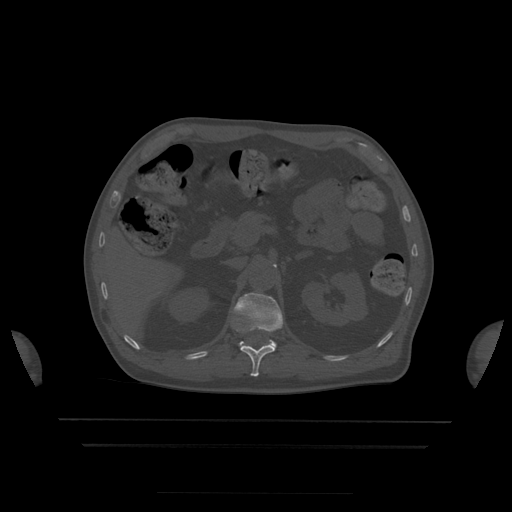
CT including the spine, one axial slice. Bone window (W 1800 / L 400 HU). 1.25 mm slice thickness. 512 × 512 image matrix, field of view 436 × 436 mm. Patient age 68 years. Case-level facts recorded for this patient, not image findings: primary cancer: urothelial.
Annotated regions visible in this slice (semi-automatic segmentation, software-assisted and operator-edited):
- L1 vertebra: bounding box [x1, y1, x2, y2] px = [232, 293, 283, 347]
- T12 vertebra: [241, 342, 276, 377]